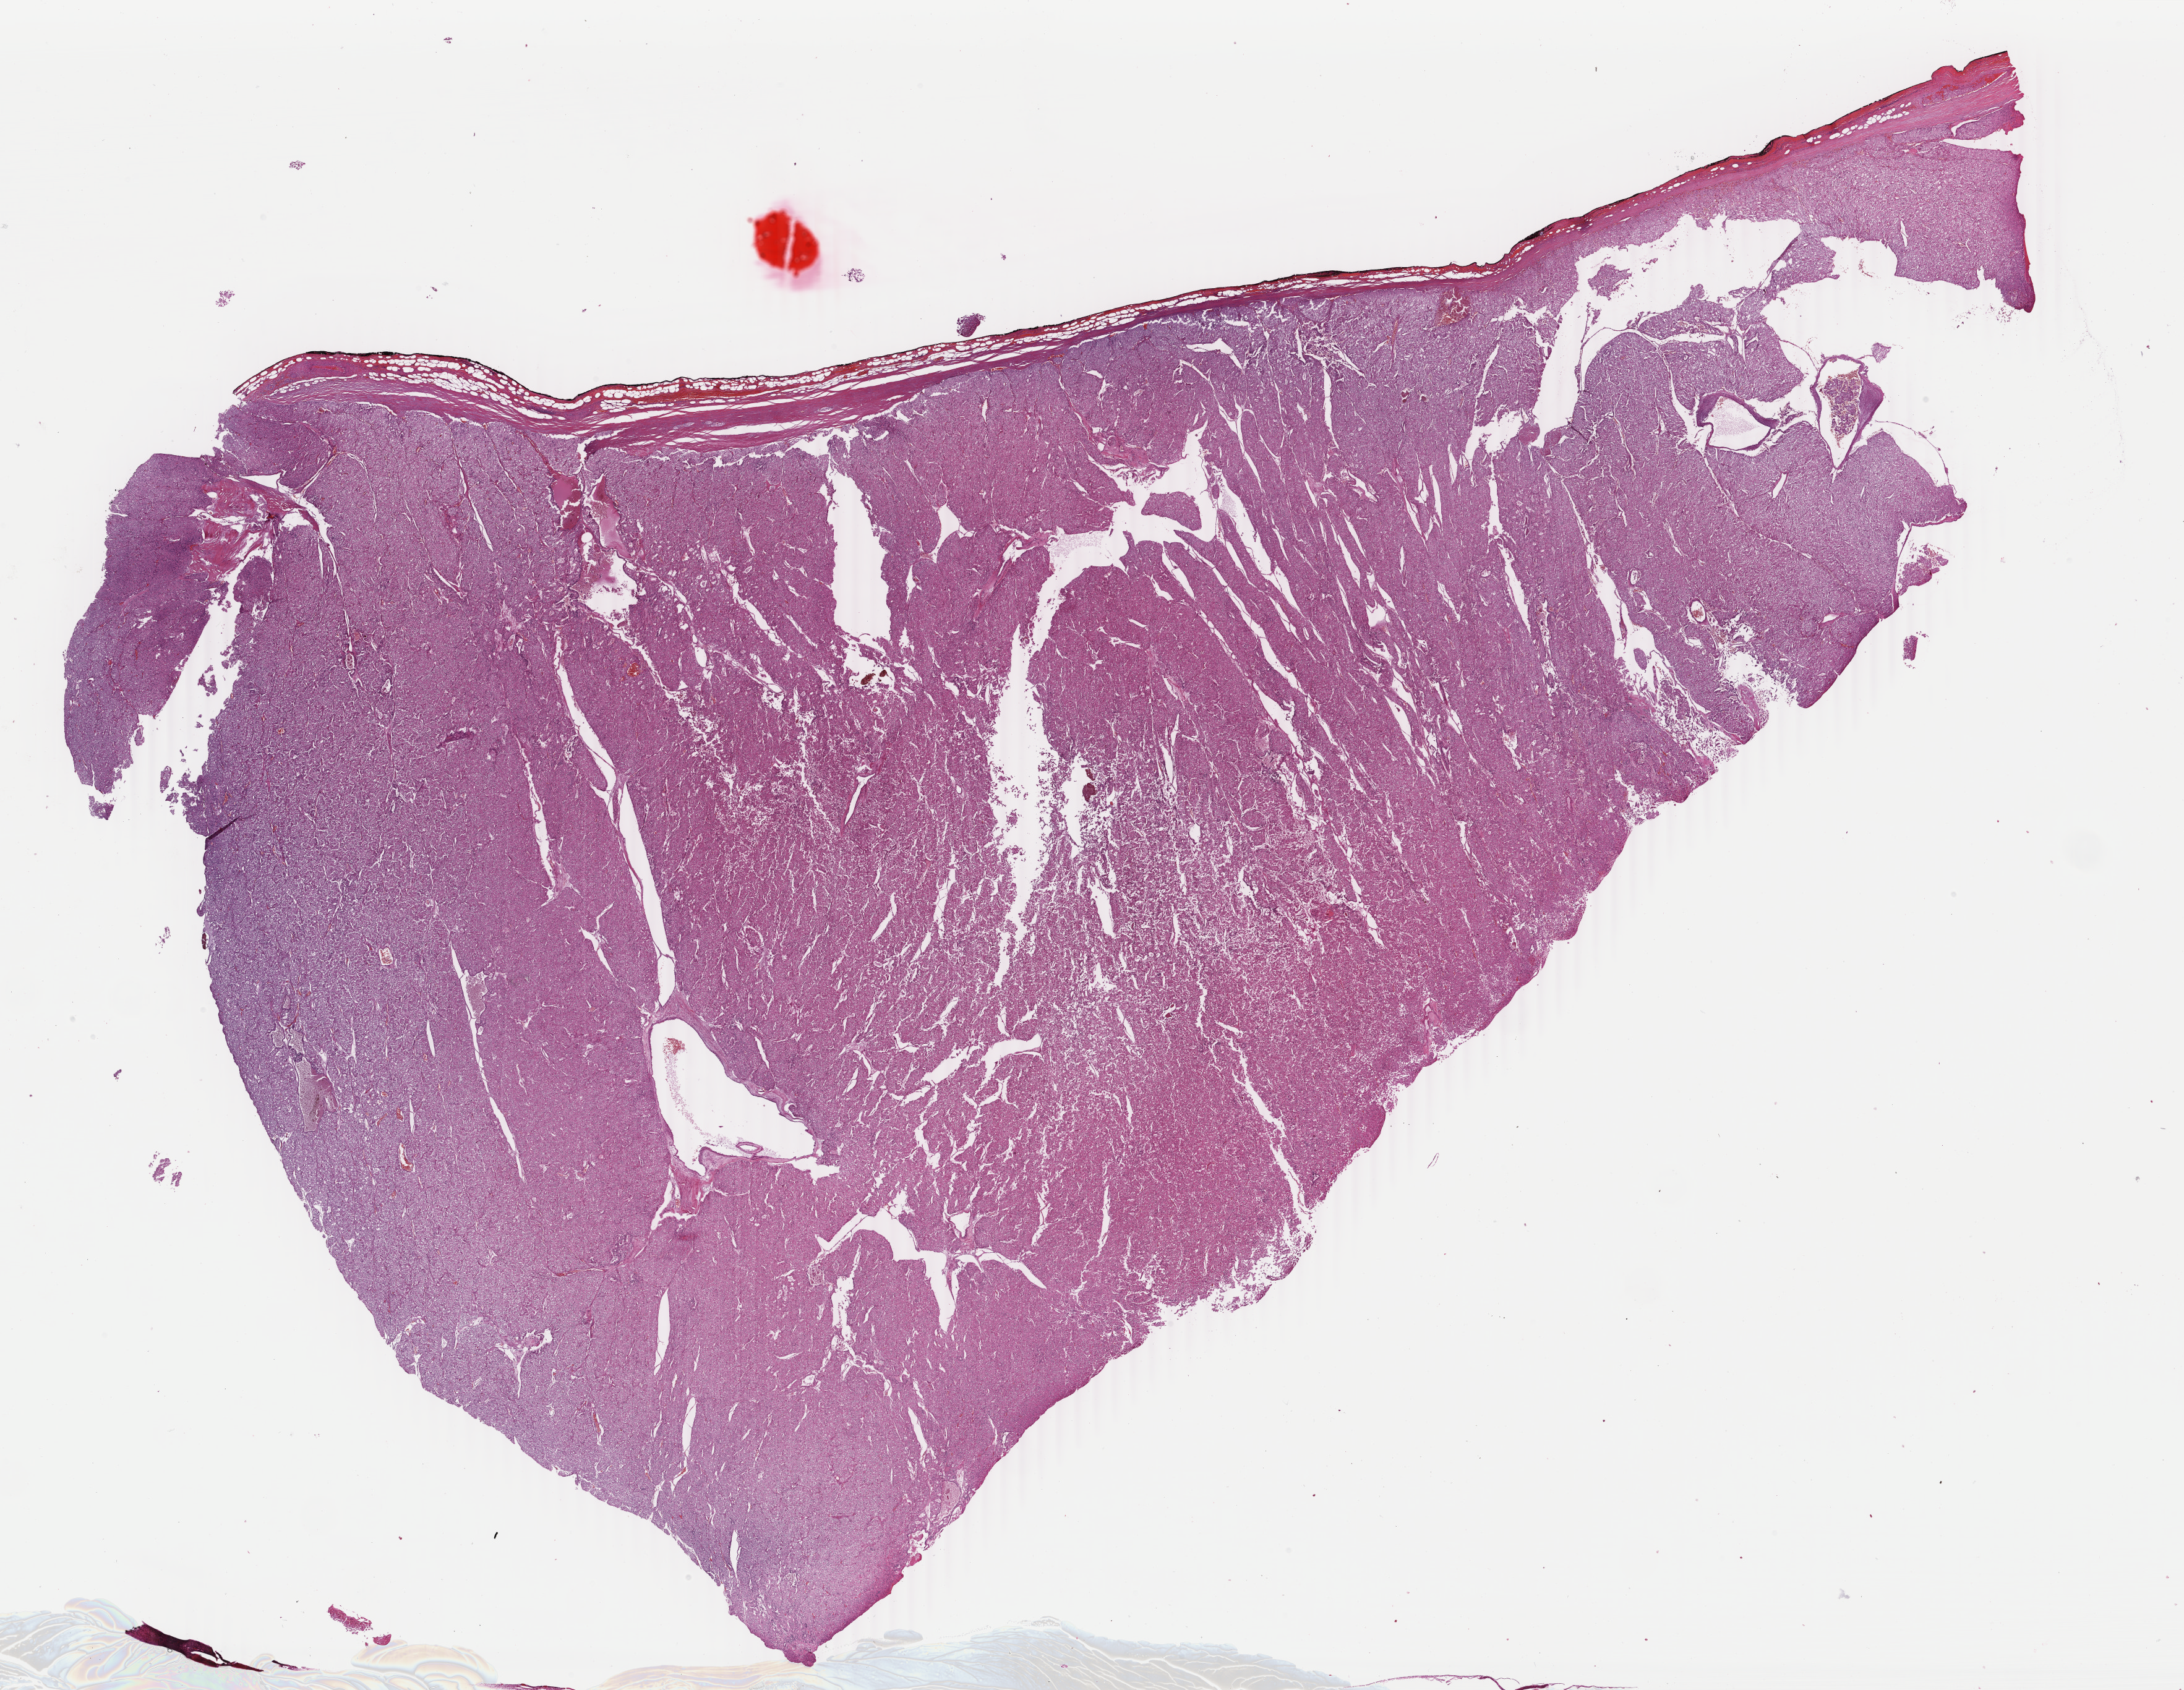
Whole-slide histology image, H&E — a low-resolution overview of the entire scanned area, about 28.1 x 21.7 mm (slide scanned at 40x). FFPE section. Primary tumour sample from the kidney. Male patient; age at initial diagnosis 57 years.
Lymph nodes positive (case pathology): 0 of 2 examined. Diagnosis: Renal cell carcinoma, chromophobe type. AJCC pathologic stage: II. Laterality: right. TNM: T2 N0 MX.